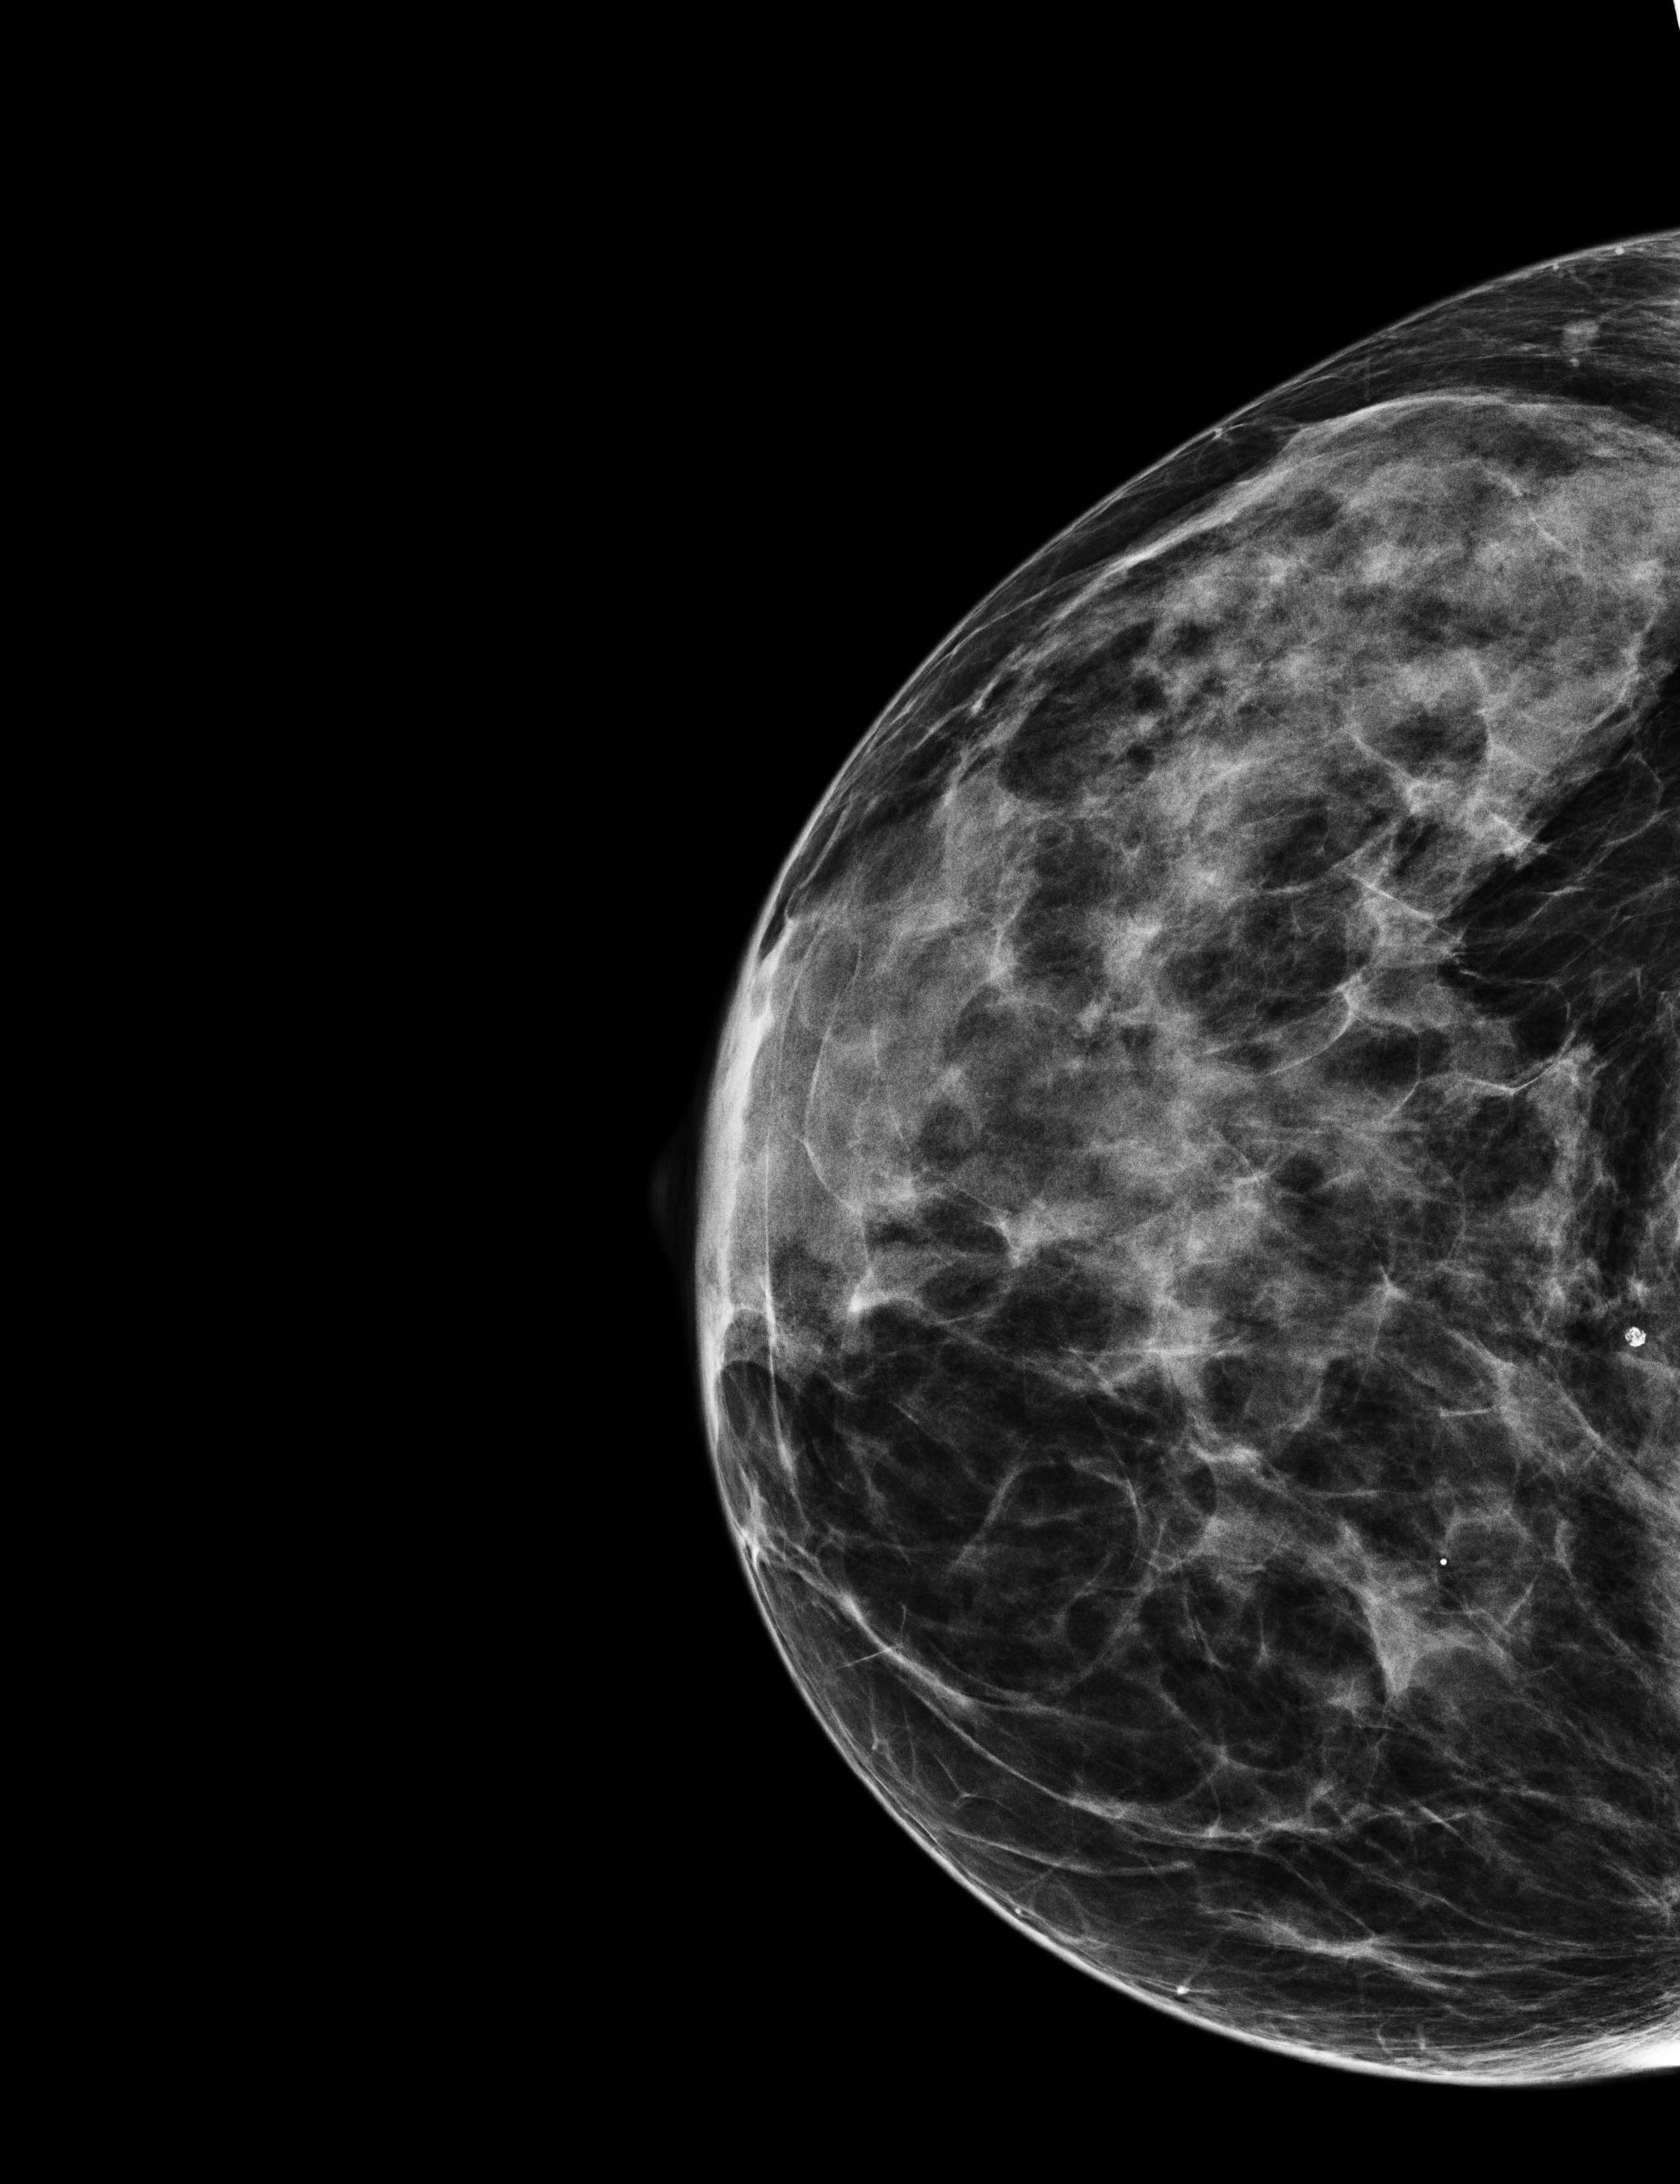
Annual screening mammography examination; compressed breast thickness 42 mm; system: Selenia Dimensions. Female patient, age 55 years.
Image type: full-field digital mammogram. Breast: right. Projection: craniocaudal (CC) view.